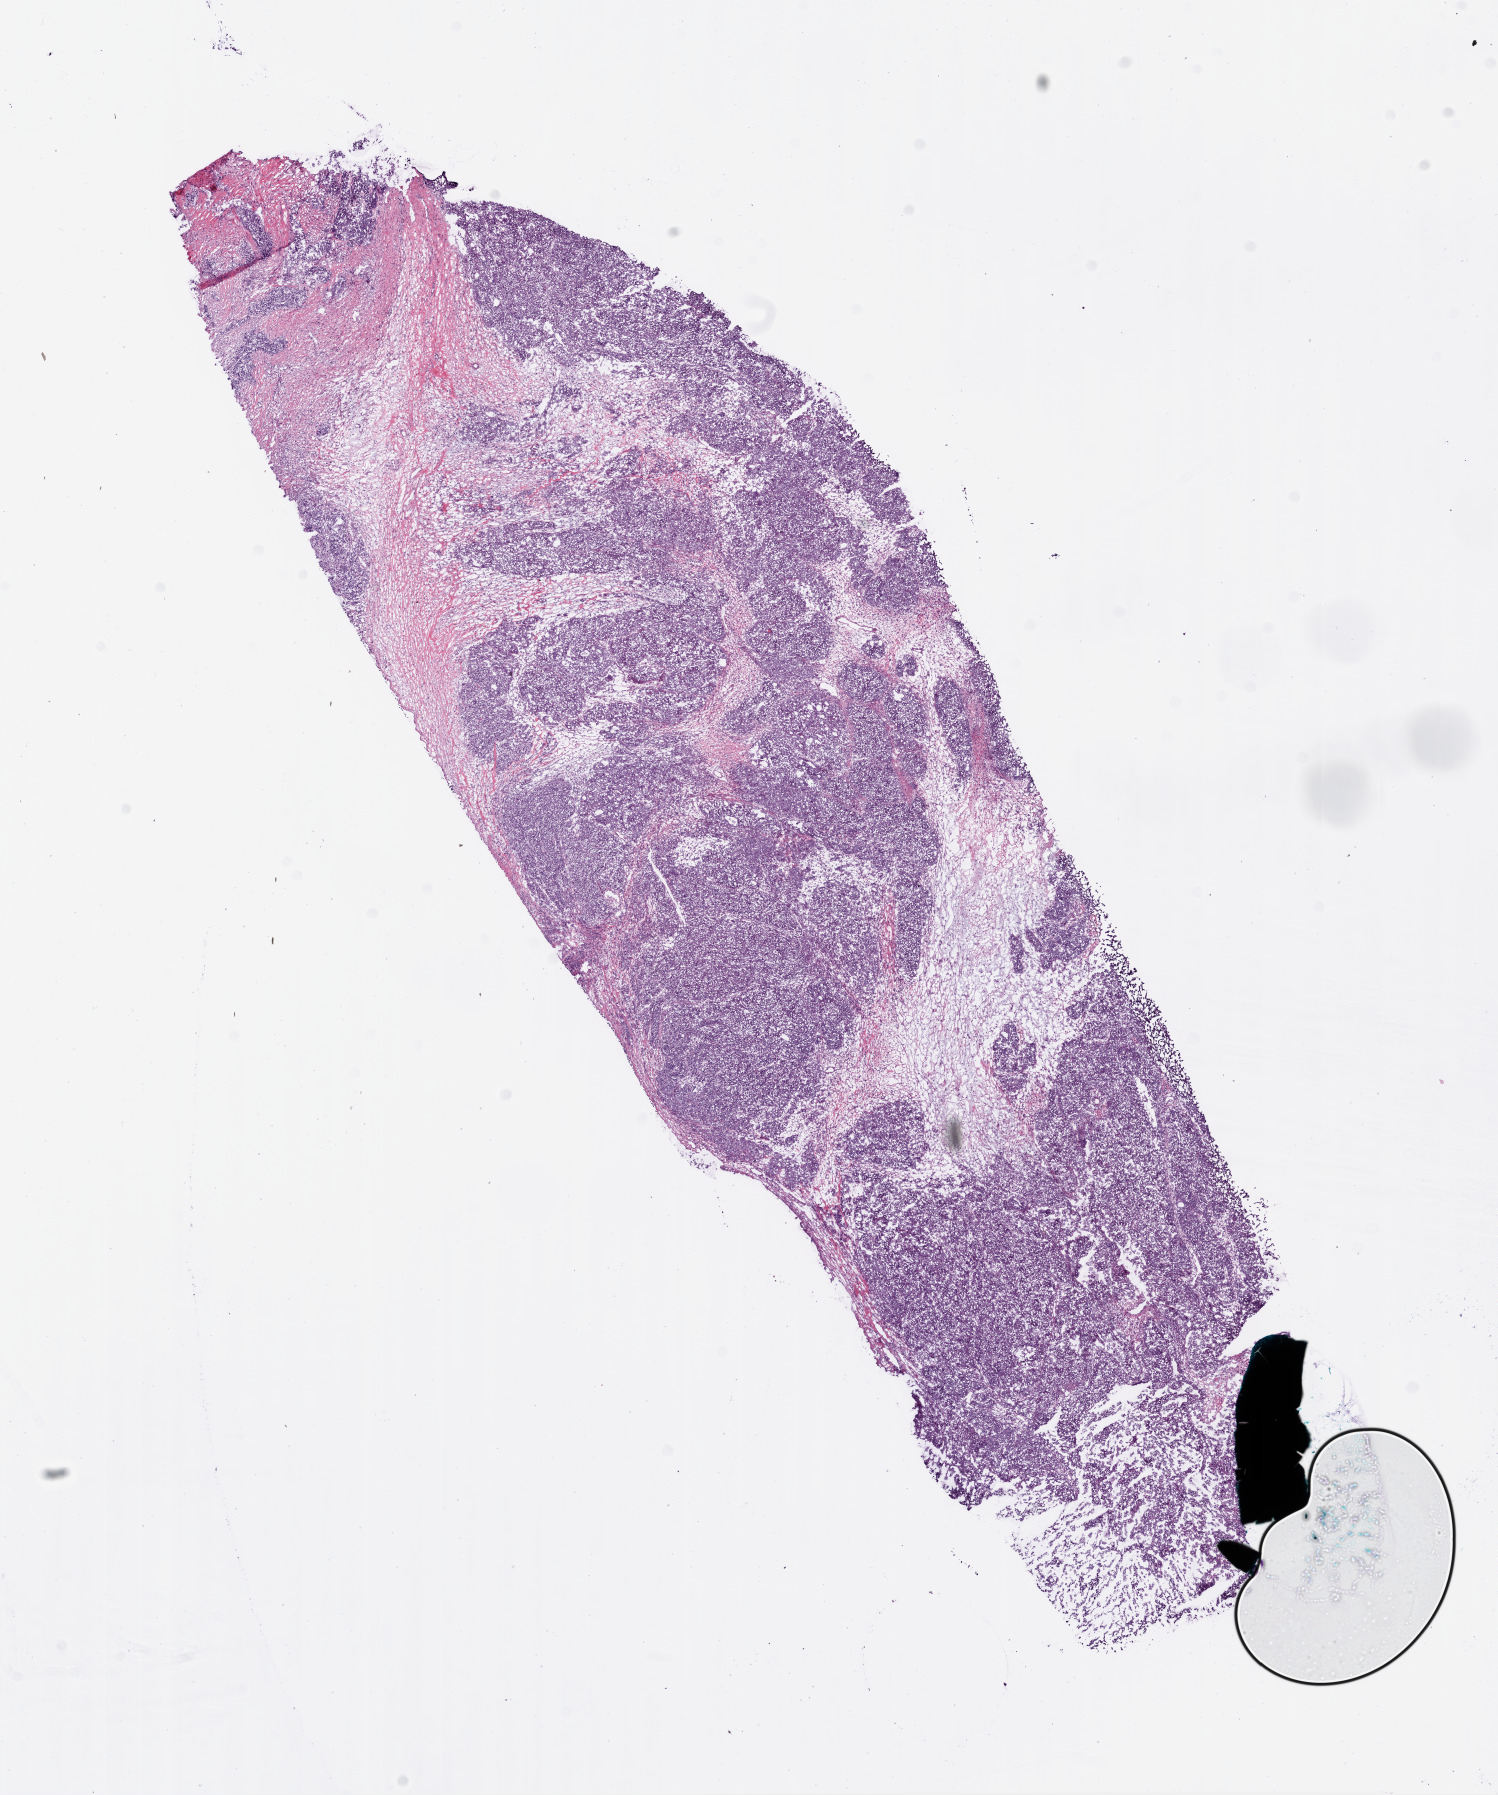
Whole-slide histology image, Hematoxylin and eosin (H&E) stained, shown as a low-resolution overview of the whole scanned area (about 12.1 x 14.5 mm). Frozen section from the bottom of the tissue portion. Sample: primary tumour, ovary. Patient: female, age at initial diagnosis 52 years. Histologic grade: G3 (poorly differentiated). Slide review estimates, as recorded: tumour cells 79%, tumour nuclei 90%, normal cells 0%, stromal cells 20%, necrosis 1%. Infiltration values recorded for this section: lymphocyte infiltration 50%.
FIGO stage: IIIB. Pathologic diagnosis: Serous cystadenocarcinoma, NOS.